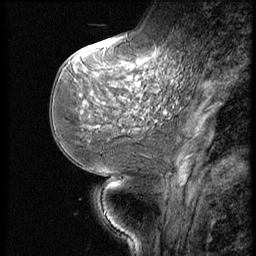
Breast MRI (dynamic contrast-enhanced), one sagittal slice; position 22 of 56 along the scan axis; dynamic contrast-enhanced series, image 2 of 3 at this slice position (ordered by acquisition); 1.5 T; TE 4.2 ms, TR 9 ms; 2.5 mm slice thickness; 256 × 256 image matrix. Patient: female, 51 years. Case-level facts recorded for this patient, not image findings: setting: breast cancer imaged before/during neoadjuvant chemotherapy; receptor status: triple-negative.
Structures marked on this image (semi-automatically segmented with operator editing):
- analysis volume of interest (the breast-tissue region the enhancement analysis was run in; not a lesion): box from (x=73, y=46) to (x=172, y=147) px
- tumour enhancement mask (voxels above the 140 % enhancement threshold inside the analysis volume of interest): (x=130, y=54)–(x=155, y=85)